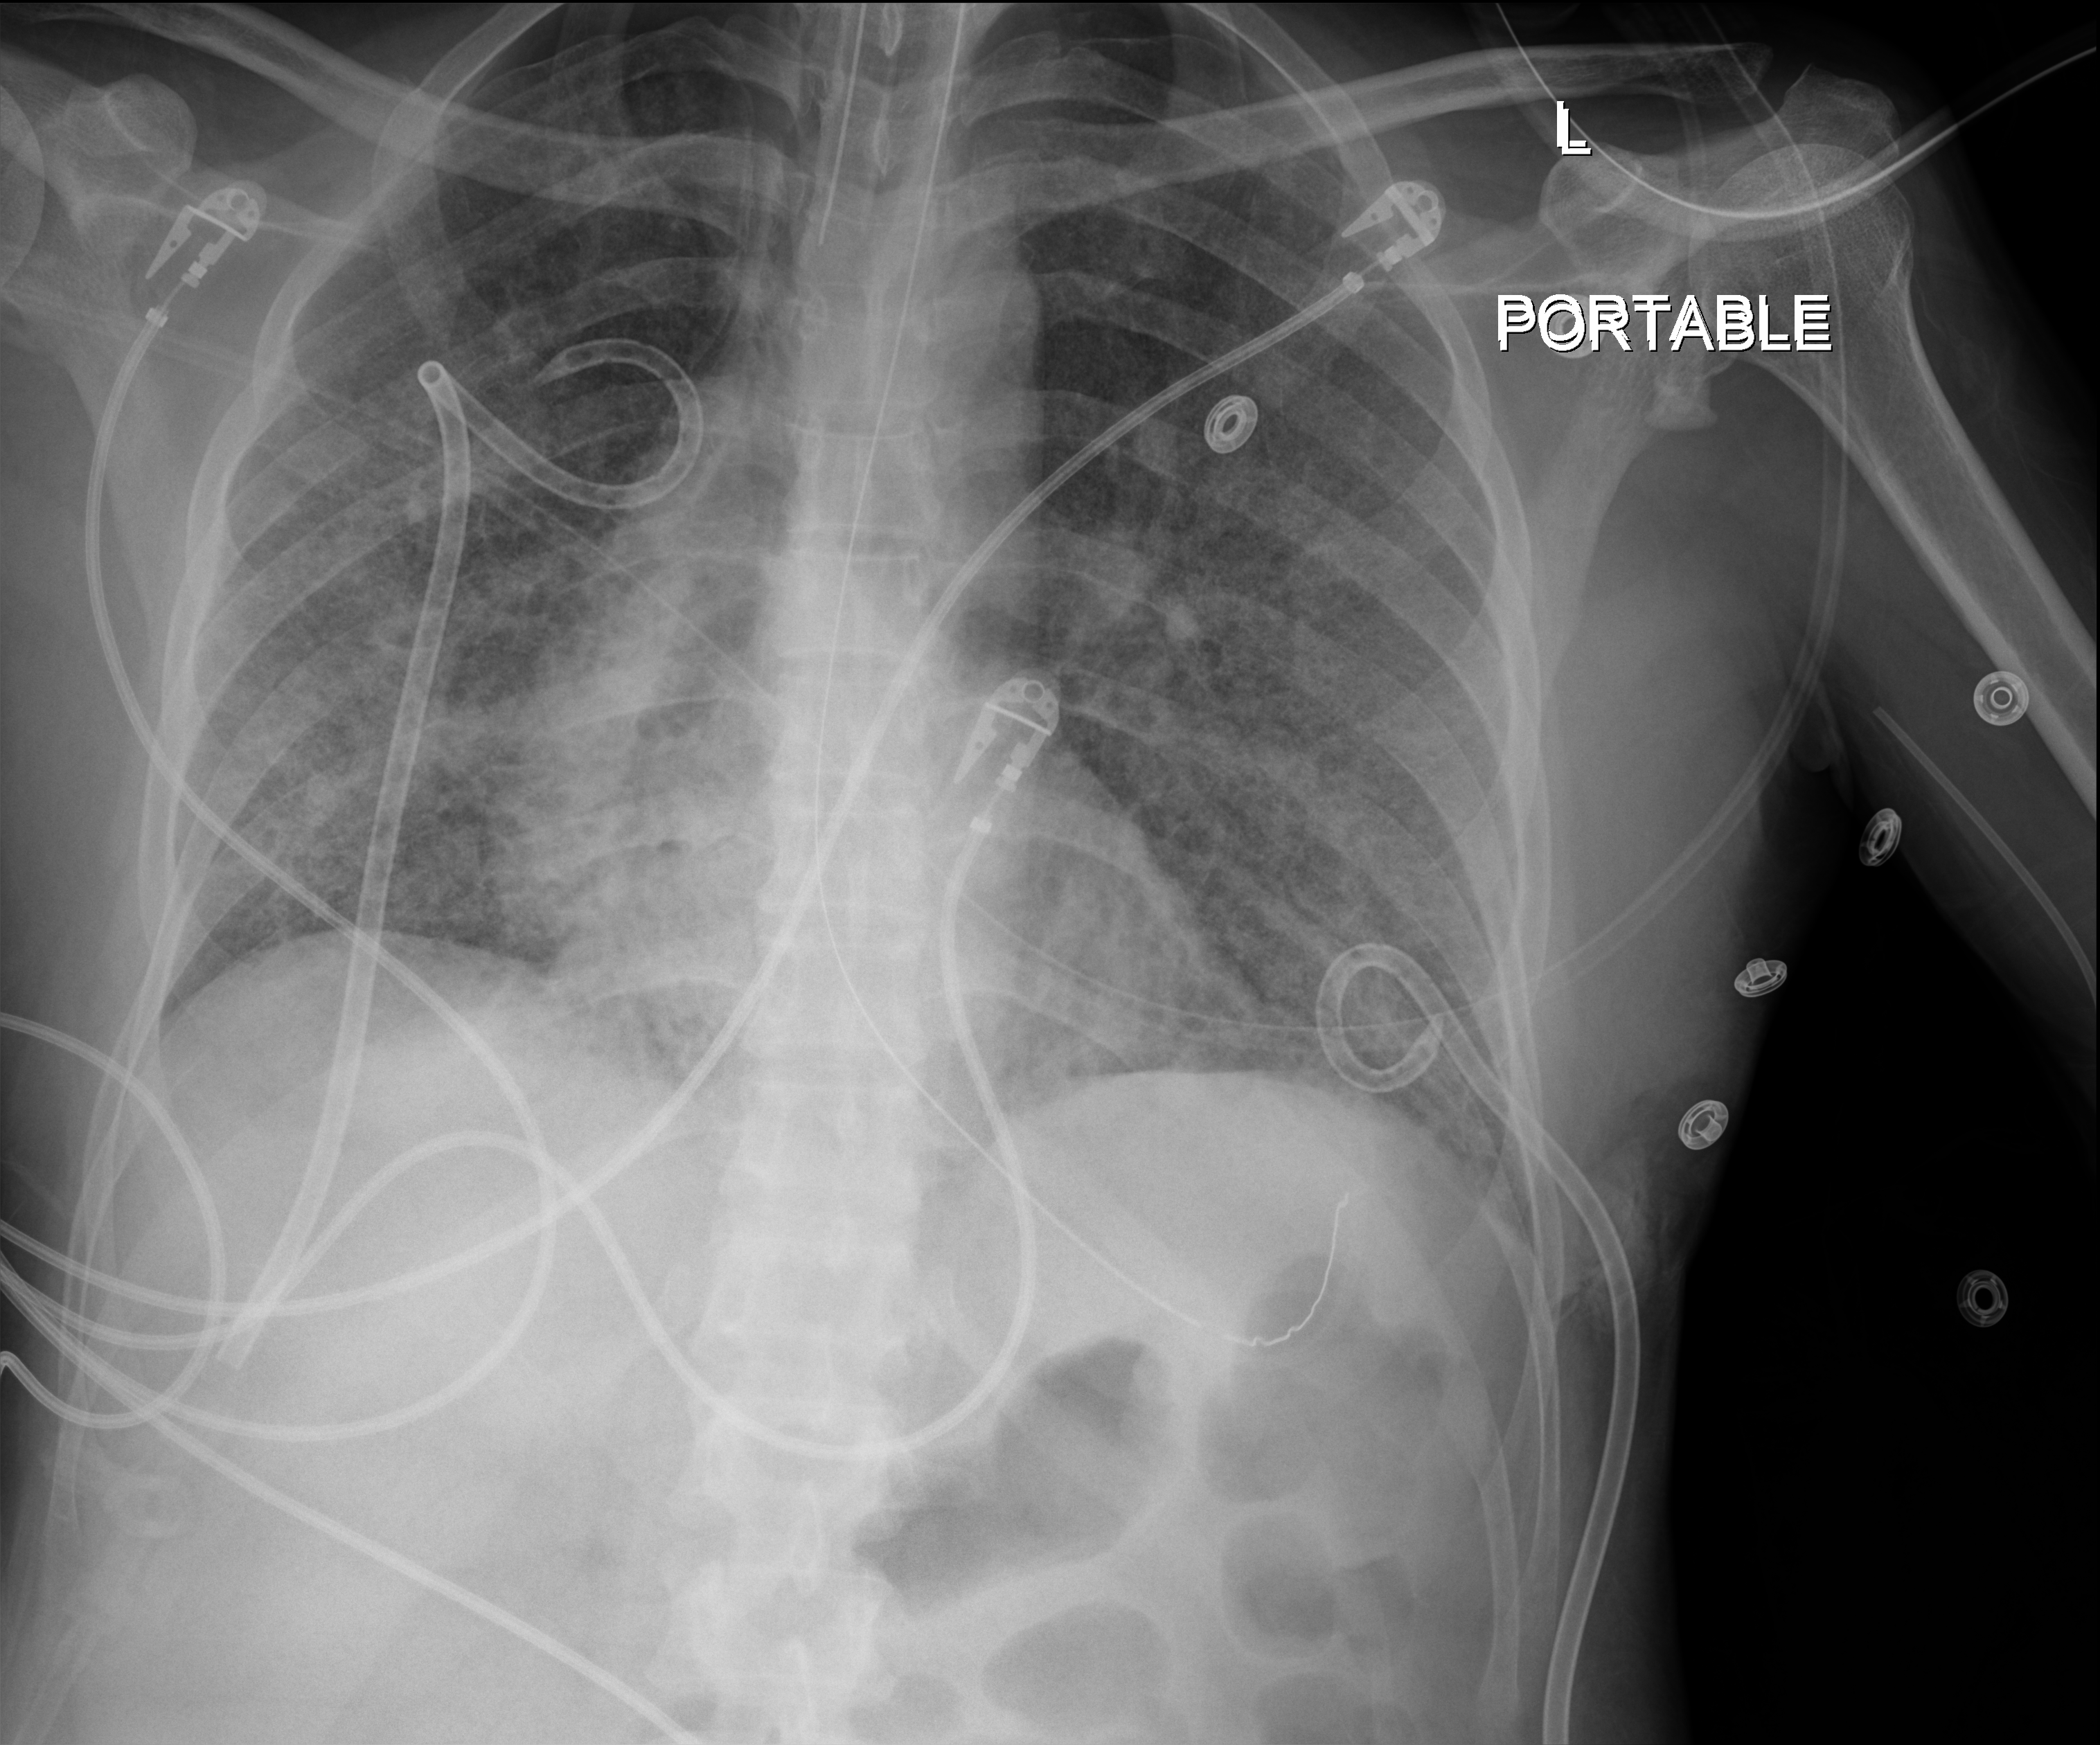
Chest X-ray. Patient hospitalised with COVID-19, aged 18–59 years.
Admission-level facts for this patient (not findings on this image; timing relative to this image not recorded): smoking status (admission record): never; mechanically ventilated during this hospital stay: yes; admitted to intensive care during this hospital stay: yes.